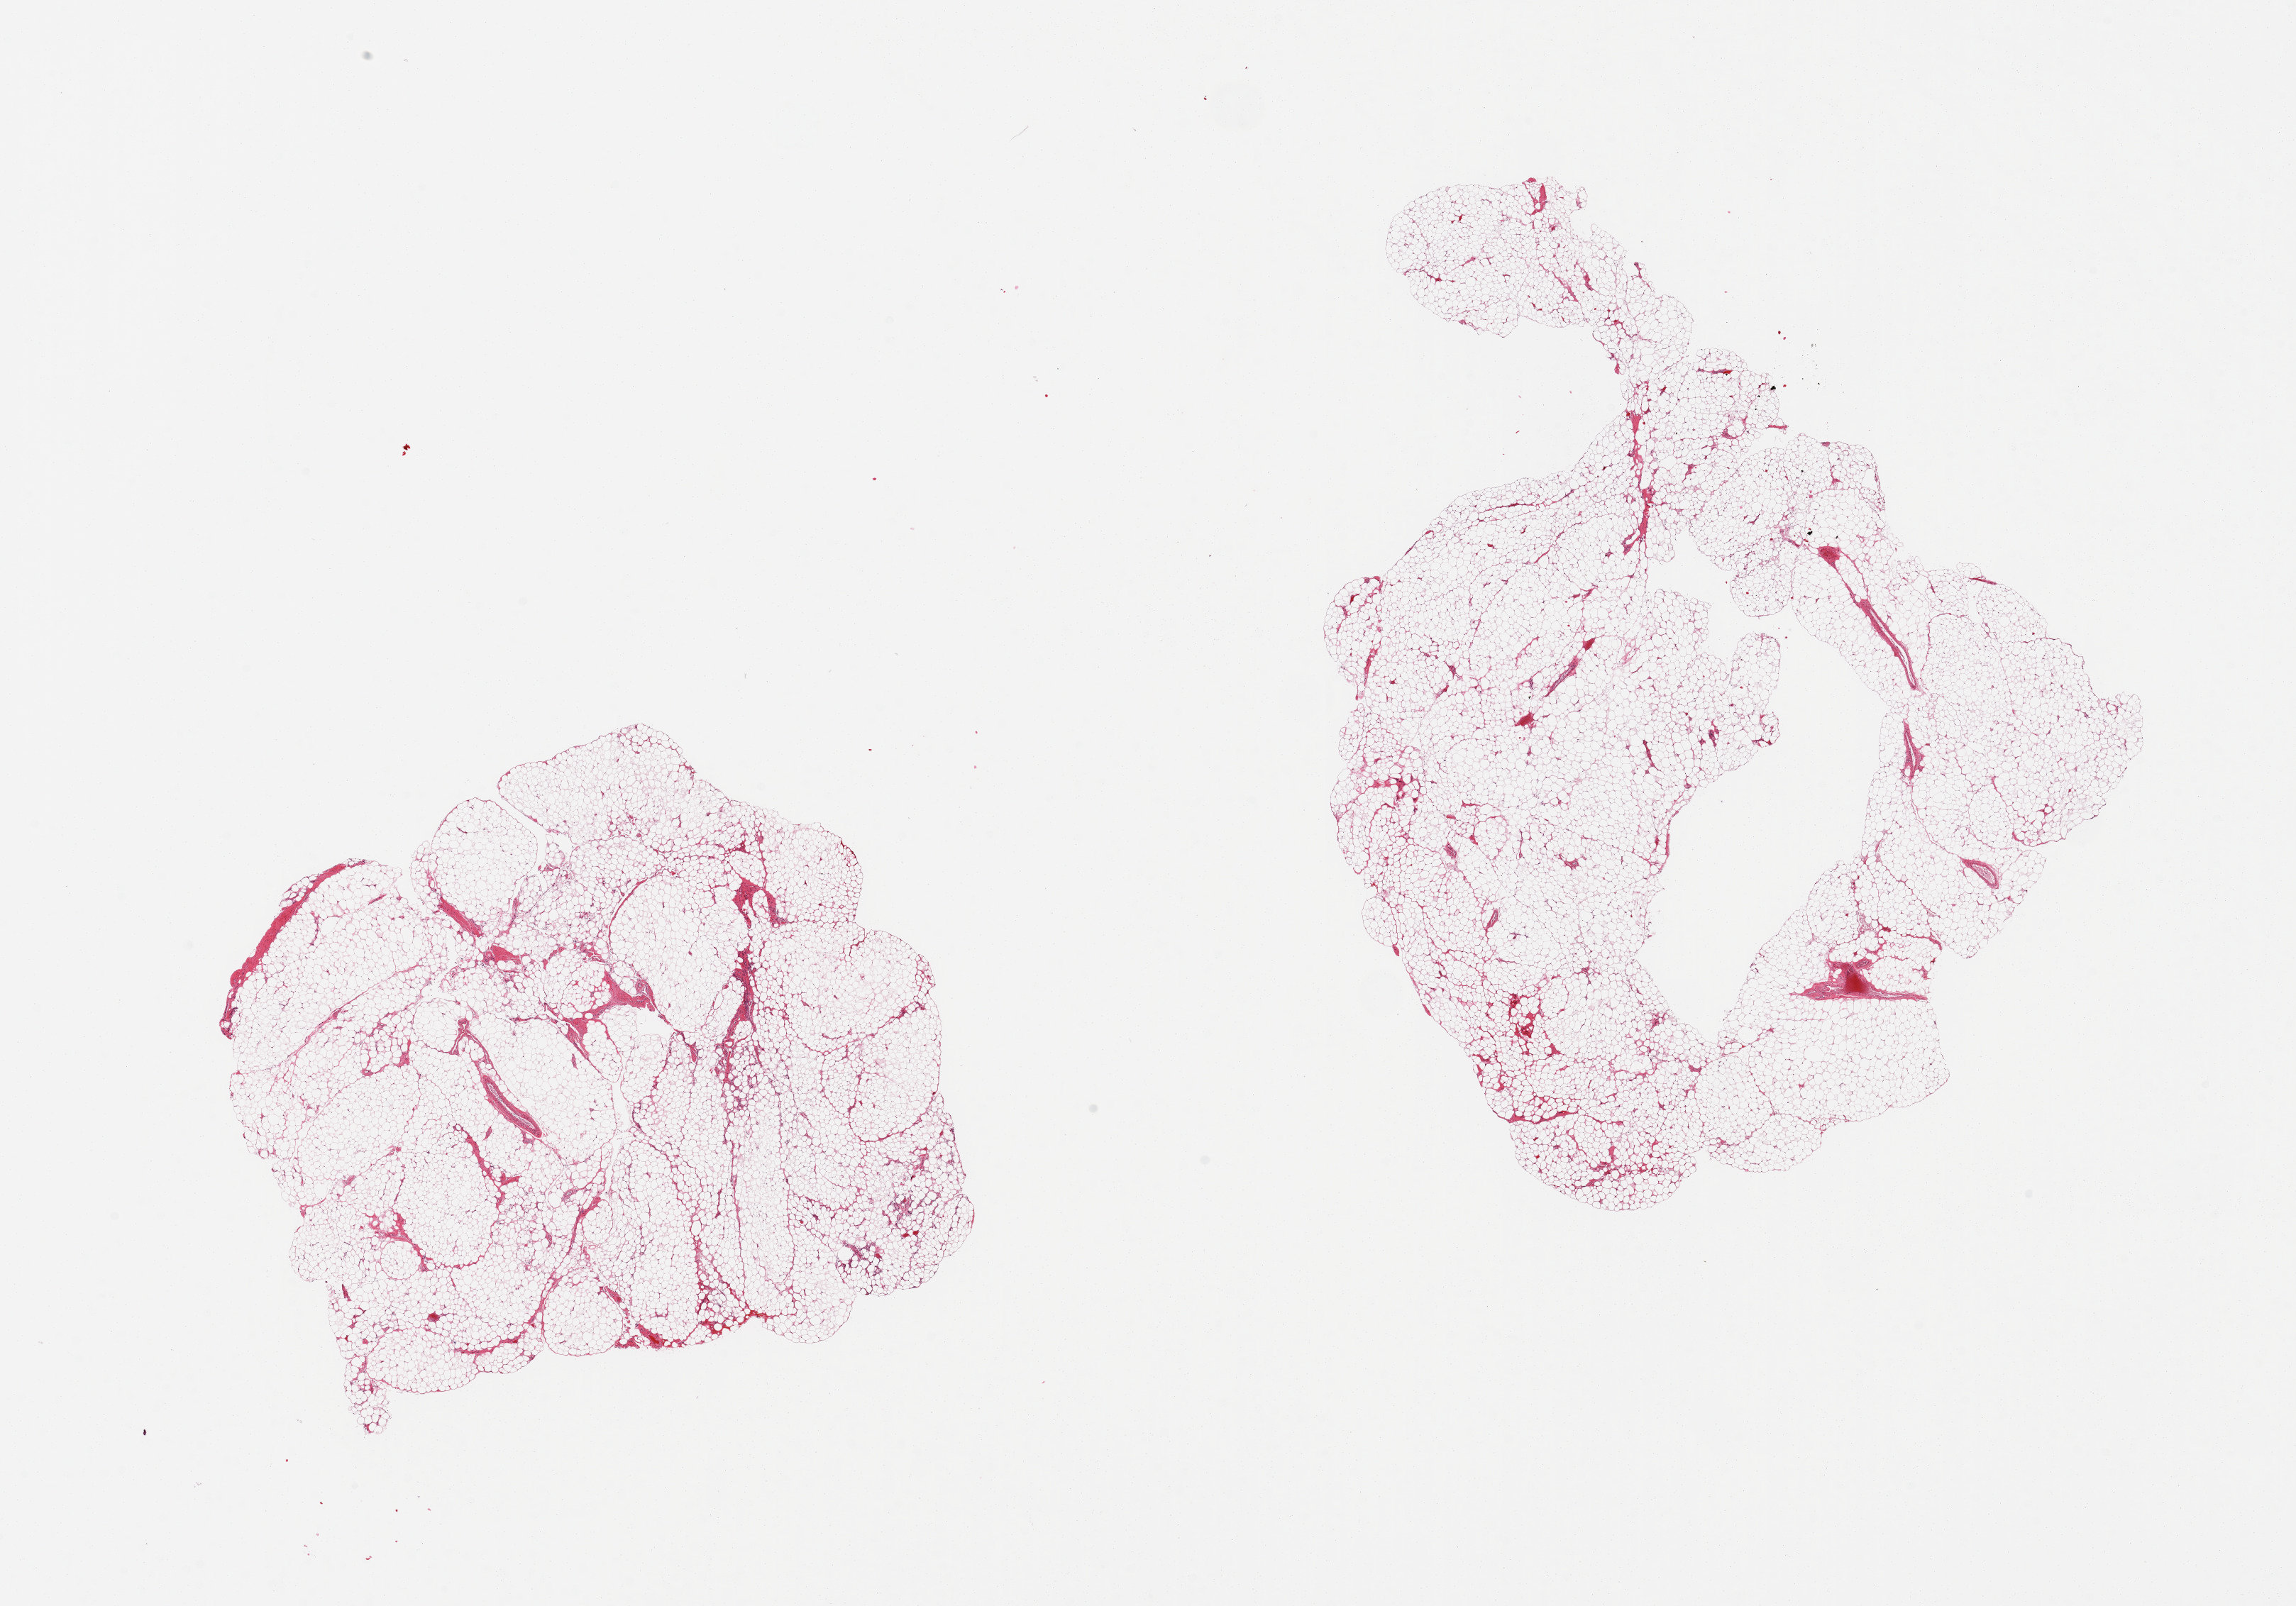
Haematoxylin and eosin whole-slide image, brightfield, whole scanned area (about 25.6 x 17.9 mm, from a 20x scan) shown as a low-resolution overview; PAXgene-fixed, paraffin-embedded tissue; target tissue: omentum; donor tissue sample.
Reviewer comment on this tissue sample: 2 pieces.